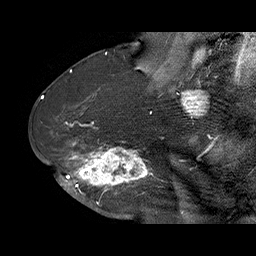
Breast MRI (dynamic contrast-enhanced), one sagittal slice; dynamic contrast-enhanced series, time point 2 of 6 at this slice position (early post-contrast); 1.5 T; TE 4.5 ms, TR 32.4 ms; 3 mm slice thickness; 256 × 256 image matrix, field of view 180 × 180 mm. Female patient. From the clinical record (not read from this slice): setting: breast cancer imaged before/during neoadjuvant chemotherapy; receptor status: HR-positive, HER2-negative.
Outlined on this slice (semi-automatically segmented with operator editing):
- analysis volume of interest (the breast-tissue region the enhancement analysis was run in; not a lesion): bounding box (x1, y1, x2, y2) in pixels: (71, 128, 159, 202)
- tumour enhancement mask (voxels above the 100 % enhancement threshold inside the analysis volume of interest): (71, 141, 153, 198)